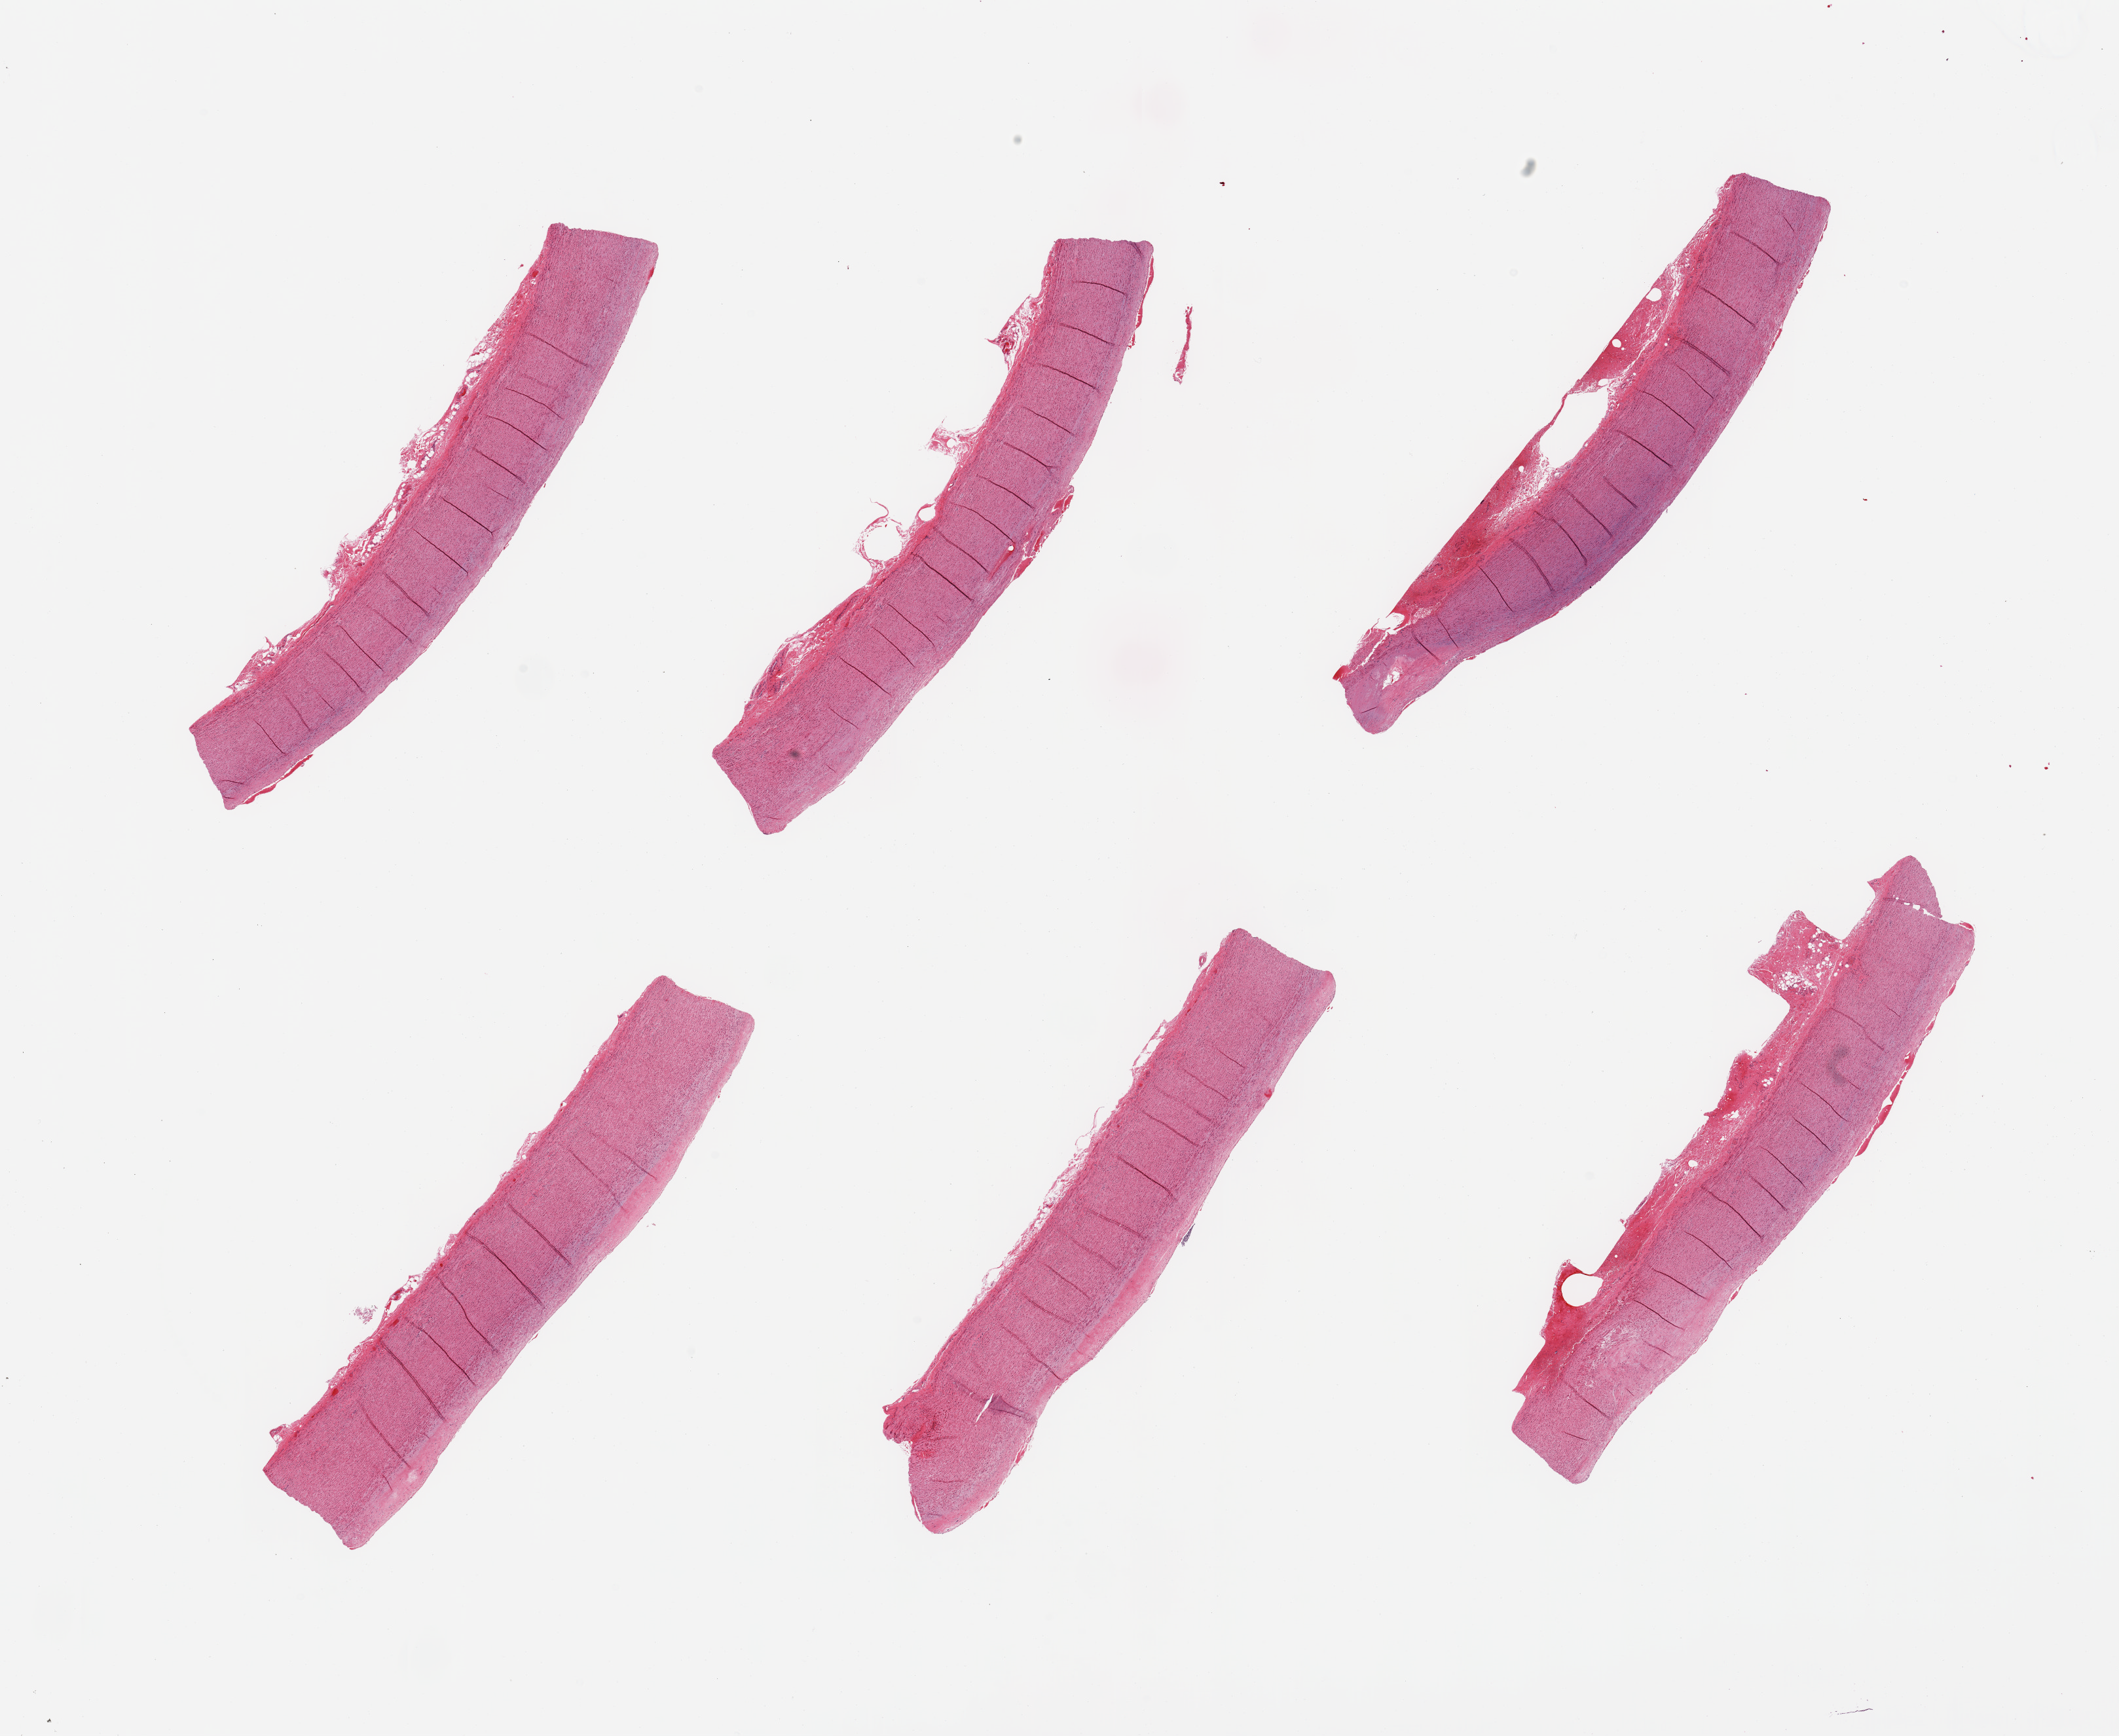
Whole-slide image, haematoxylin and eosin stain, brightfield — a low-resolution overview of the entire scanned area, about 25.6 x 21.0 mm; PAXgene-fixed paraffin-embedded (PFPE) section; section of aorta (target tissue); donor tissue sample. Male donor.
* reviewer comment on this tissue sample: 6 pieces; no plaques; up to 0.6 mm adventitial fibrous tissue